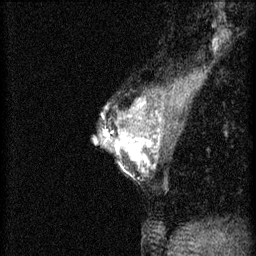
Breast MRI (dynamic contrast-enhanced), one sagittal slice. Position 34 of 46 along the scan axis. 3 images stored at this slice position (order not interpretable as contrast timing). 1.5 T. TE 4.2 ms, TR 8.2 ms. 2 mm slice thickness. 256 × 256 image matrix, field of view 180 × 180 mm. Female patient, age 44 years.
Outlined on this slice (semi-automatically segmented with operator editing):
- analysis volume of interest (the breast-tissue region the enhancement analysis was run in; not a lesion): box from (x=110, y=128) to (x=156, y=177) px
- tumour enhancement mask (voxels above the 70 % enhancement threshold inside the analysis volume of interest): (x=110, y=132)–(x=156, y=173)